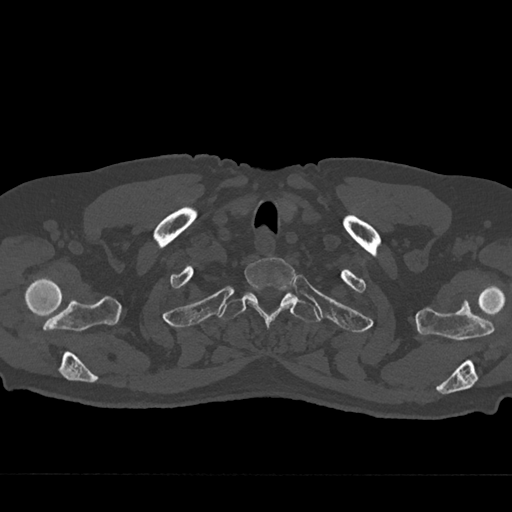
CT including the spine, one axial slice; reconstruction kernel Br40s/3; 120 kVp; bone window (W 1800 / L 400 HU); 0.5 mm slice thickness; 512 × 512 image matrix, field of view 377 × 377 mm. Patient: male, 75 years. Case-level facts recorded for this patient, not image findings: primary cancer: renal.
Structures marked on this image (semi-automatic segmentation, software-assisted and operator-edited):
- T1 vertebra: bounding box (x1, y1, x2, y2) in pixels: (245, 257, 295, 326)
- T2 vertebra: (219, 289, 320, 323)